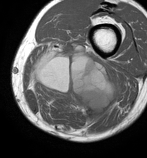
MRI of an extremity soft-tissue mass, one axial slice. Position 30 of 86 along the scan axis. MR volume resampled by the dataset authors to the PET/CT grid (not the native acquisition matrix). 3.27 mm slice thickness. 147 × 158 image matrix, field of view 144 × 154 mm. Male patient. Case-level facts recorded for this patient, not image findings: histological type: undifferentiated pleomorphic liposarcoma; grade: high; site of the primary tumour: left thigh.
Annotated regions visible in this slice (expert contour drawn on MRI and transferred to this co-registered scan by the dataset authors):
- gross tumour volume including surrounding oedema: bounding box [x1, y1, x2, y2] px = [28, 42, 120, 125]
- gross tumour volume (mass): [37, 56, 113, 114]